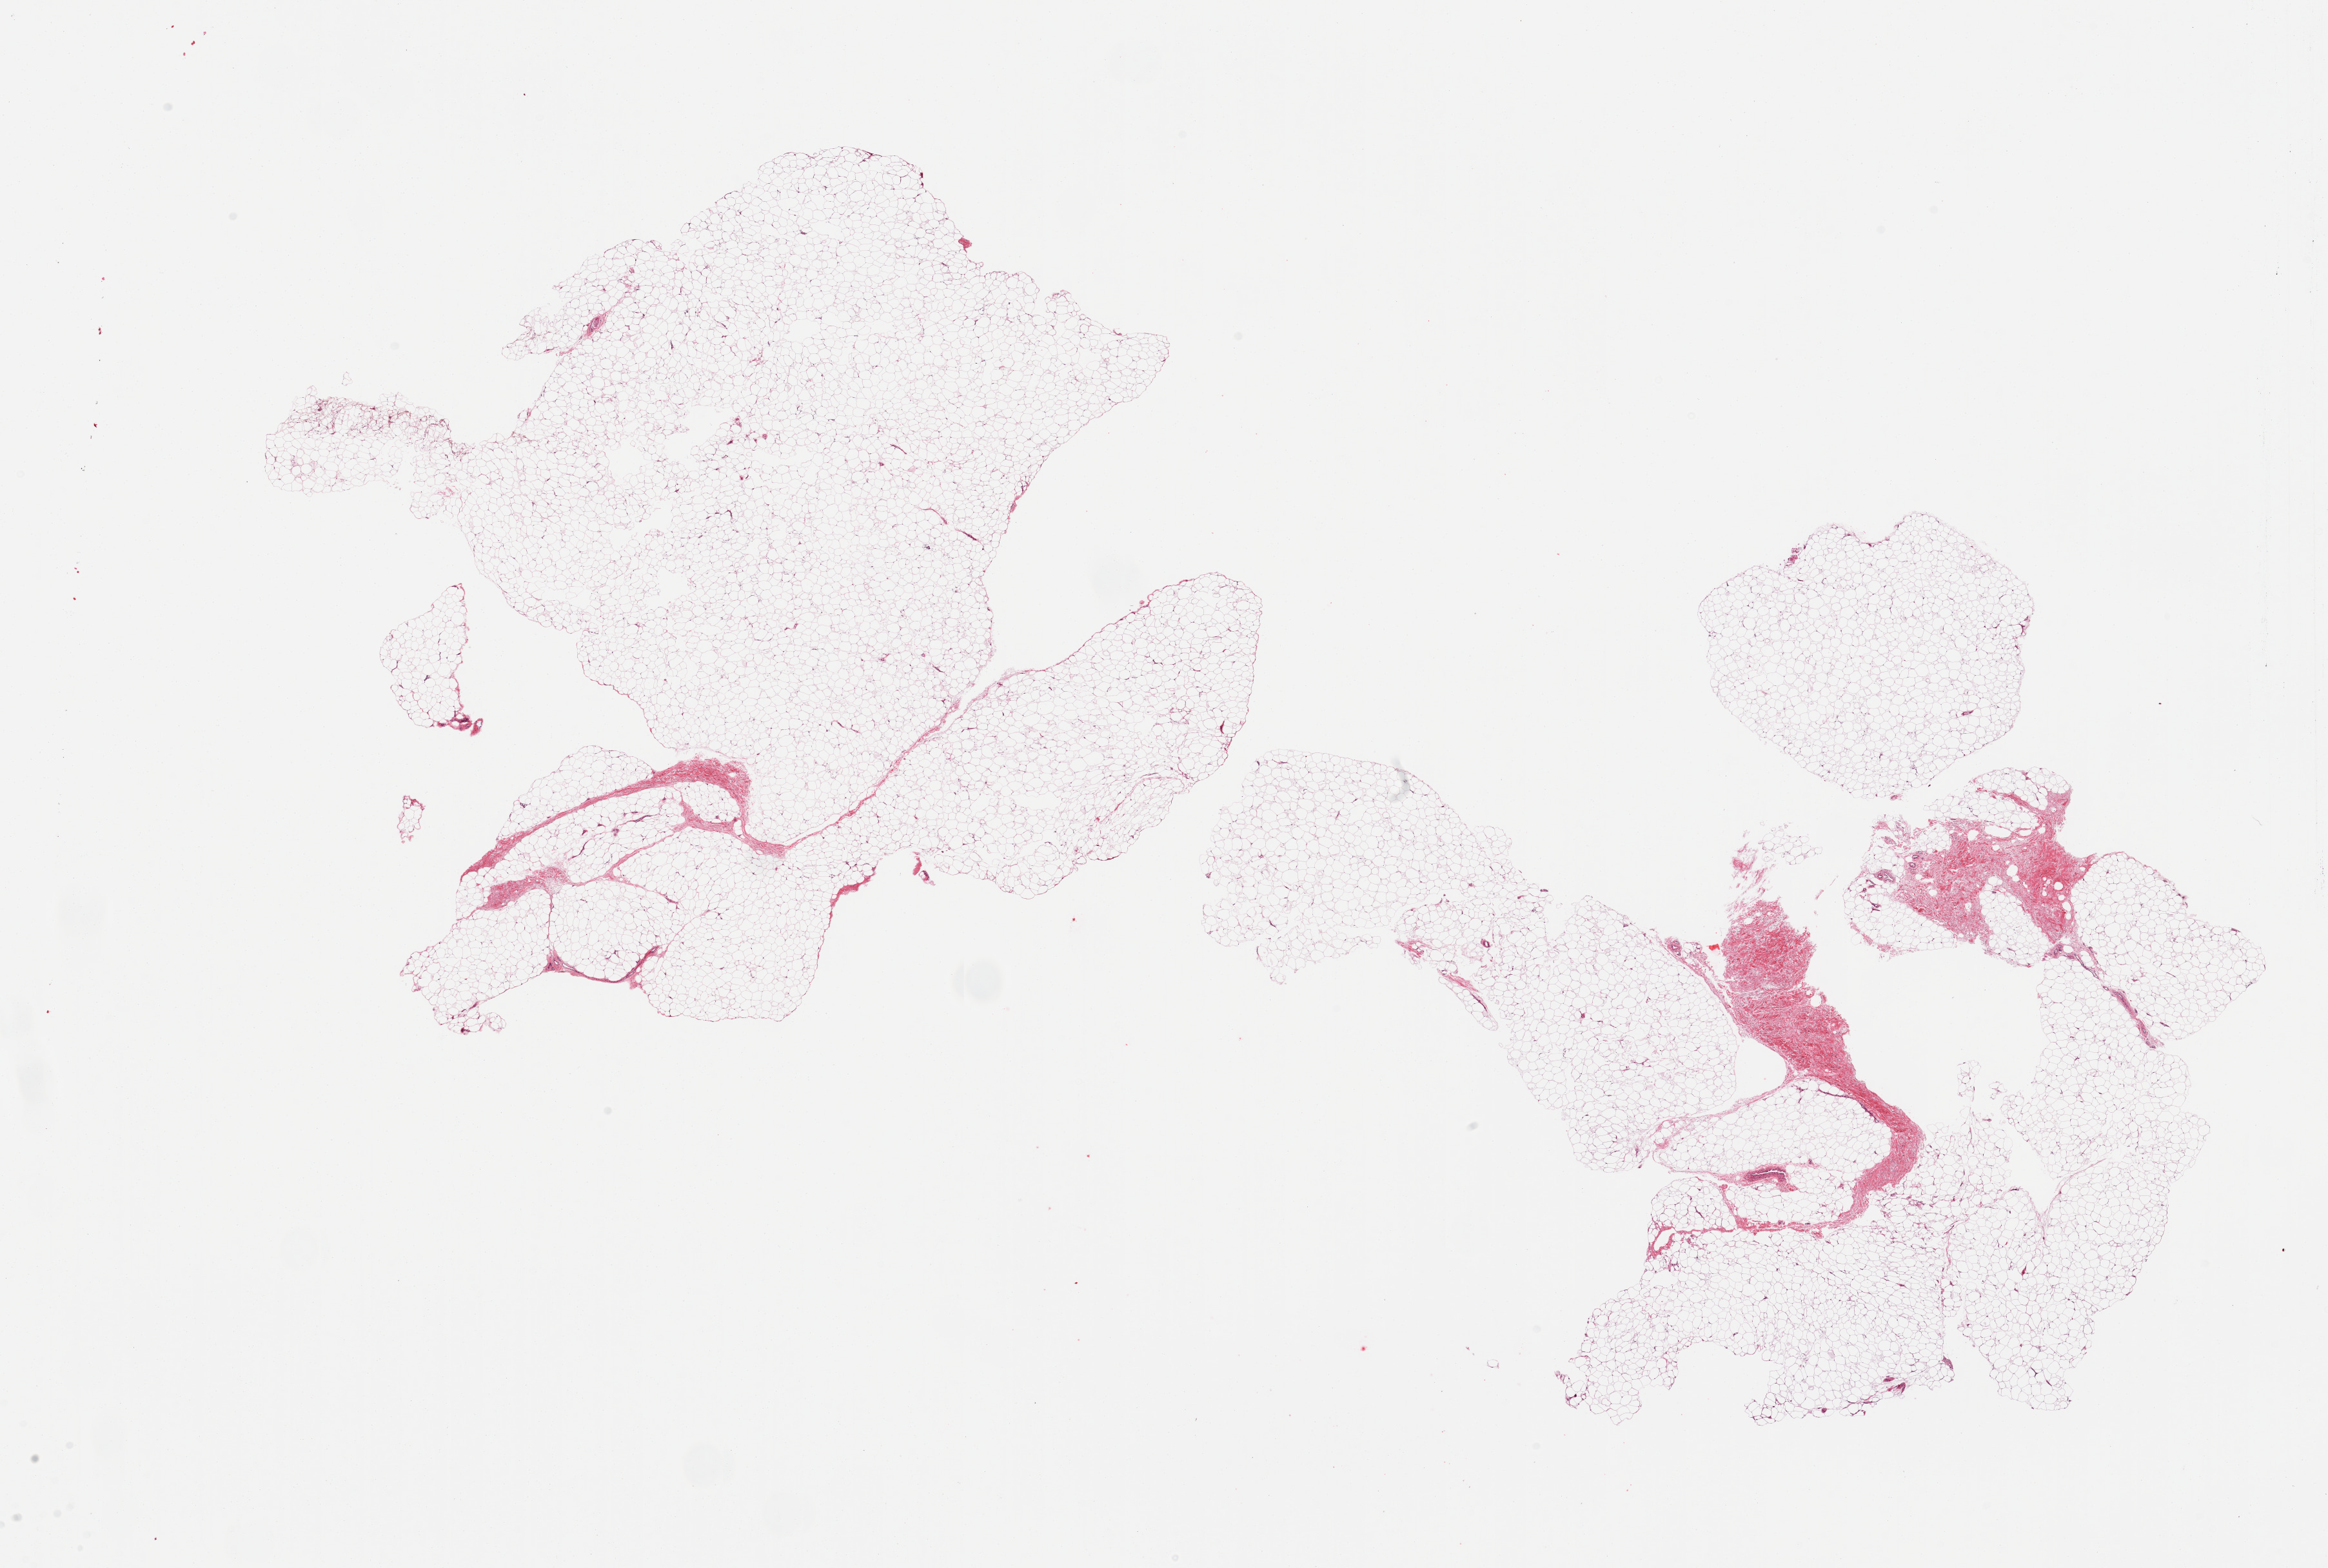
Digitized haematoxylin and eosin-stained section — shown as a low-resolution overview of the whole scanned area (about 28.5 x 19.2 mm, acquisition: 20x scan), PAXgene-fixed paraffin-embedded (PFPE) section, sampled site (target tissue): adipose tissue, donor tissue sample. Donor: male.
Pathologist's review note for this sample: 2 pieces, ~10% fascia.